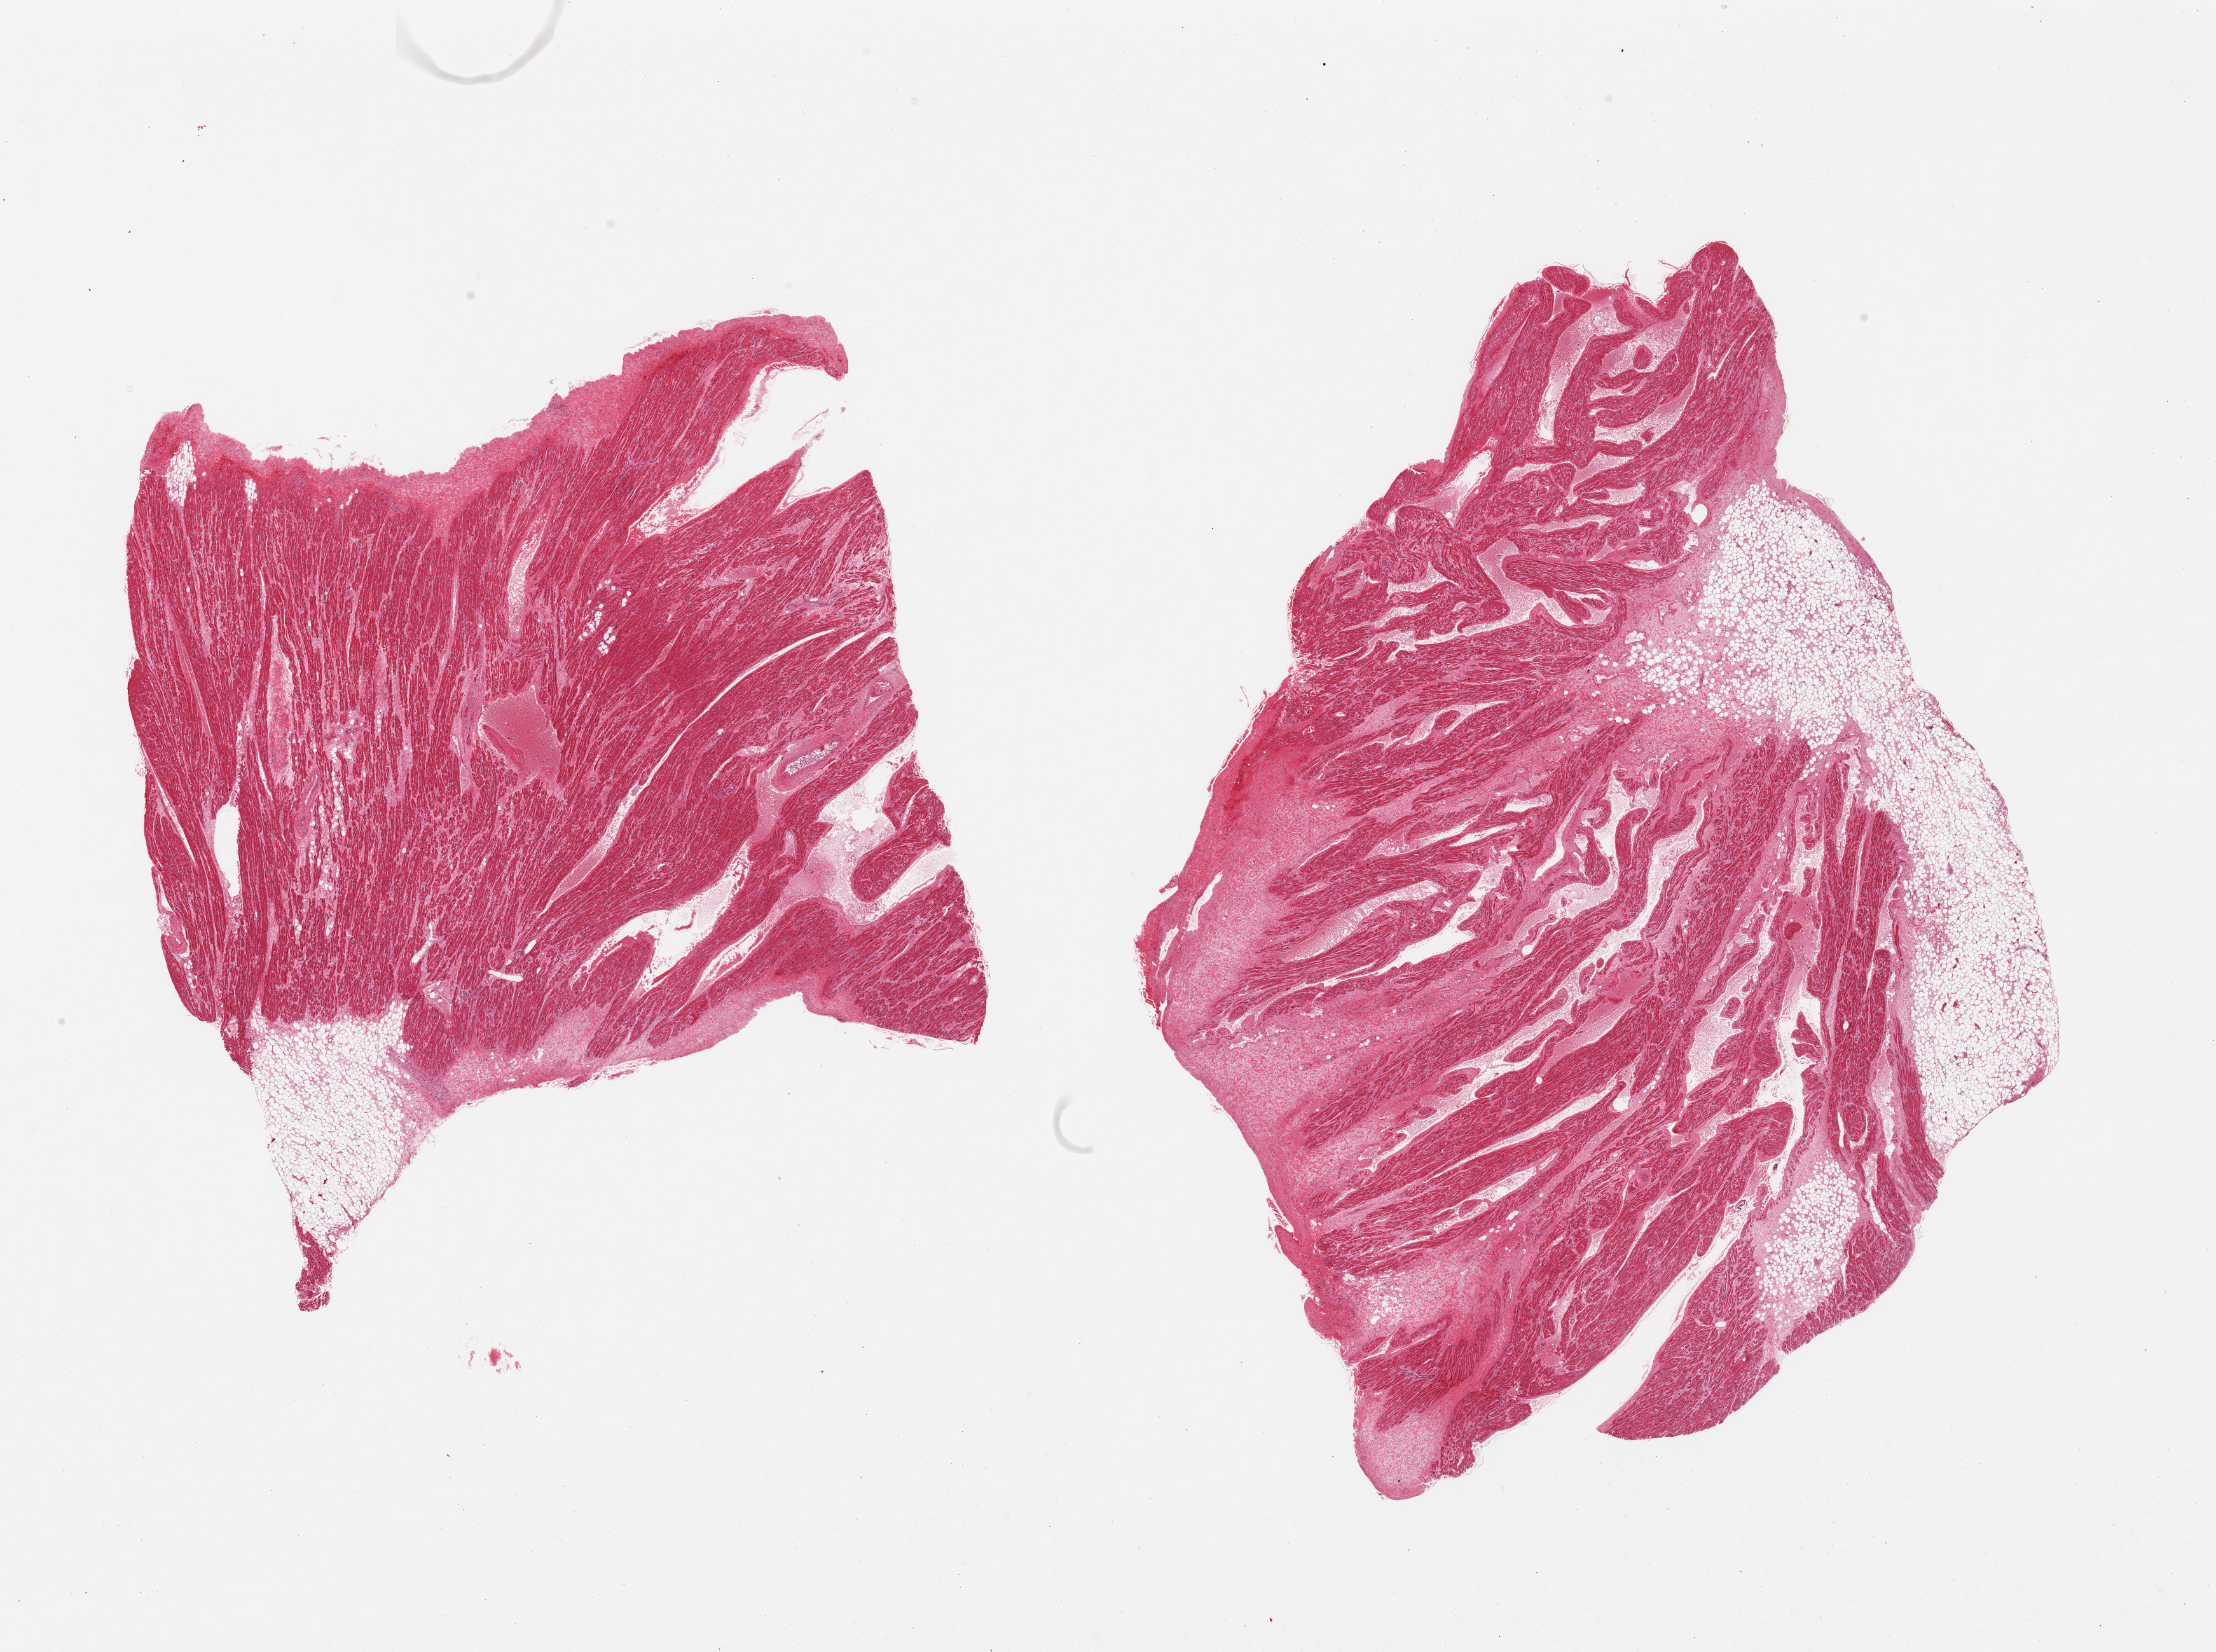
Digitized H&E-stained section, low-resolution overview of the scanned area, about 27.6 x 20.5 mm (slide scanned at 20x). PAXgene-fixed paraffin-embedded (PFPE) section. Target tissue: auricular appendage. Tissue donor sample. Donor sex: male.
Pathologist's review note for this sample: 2 pieces; 40% & 10% fibrofatty content.